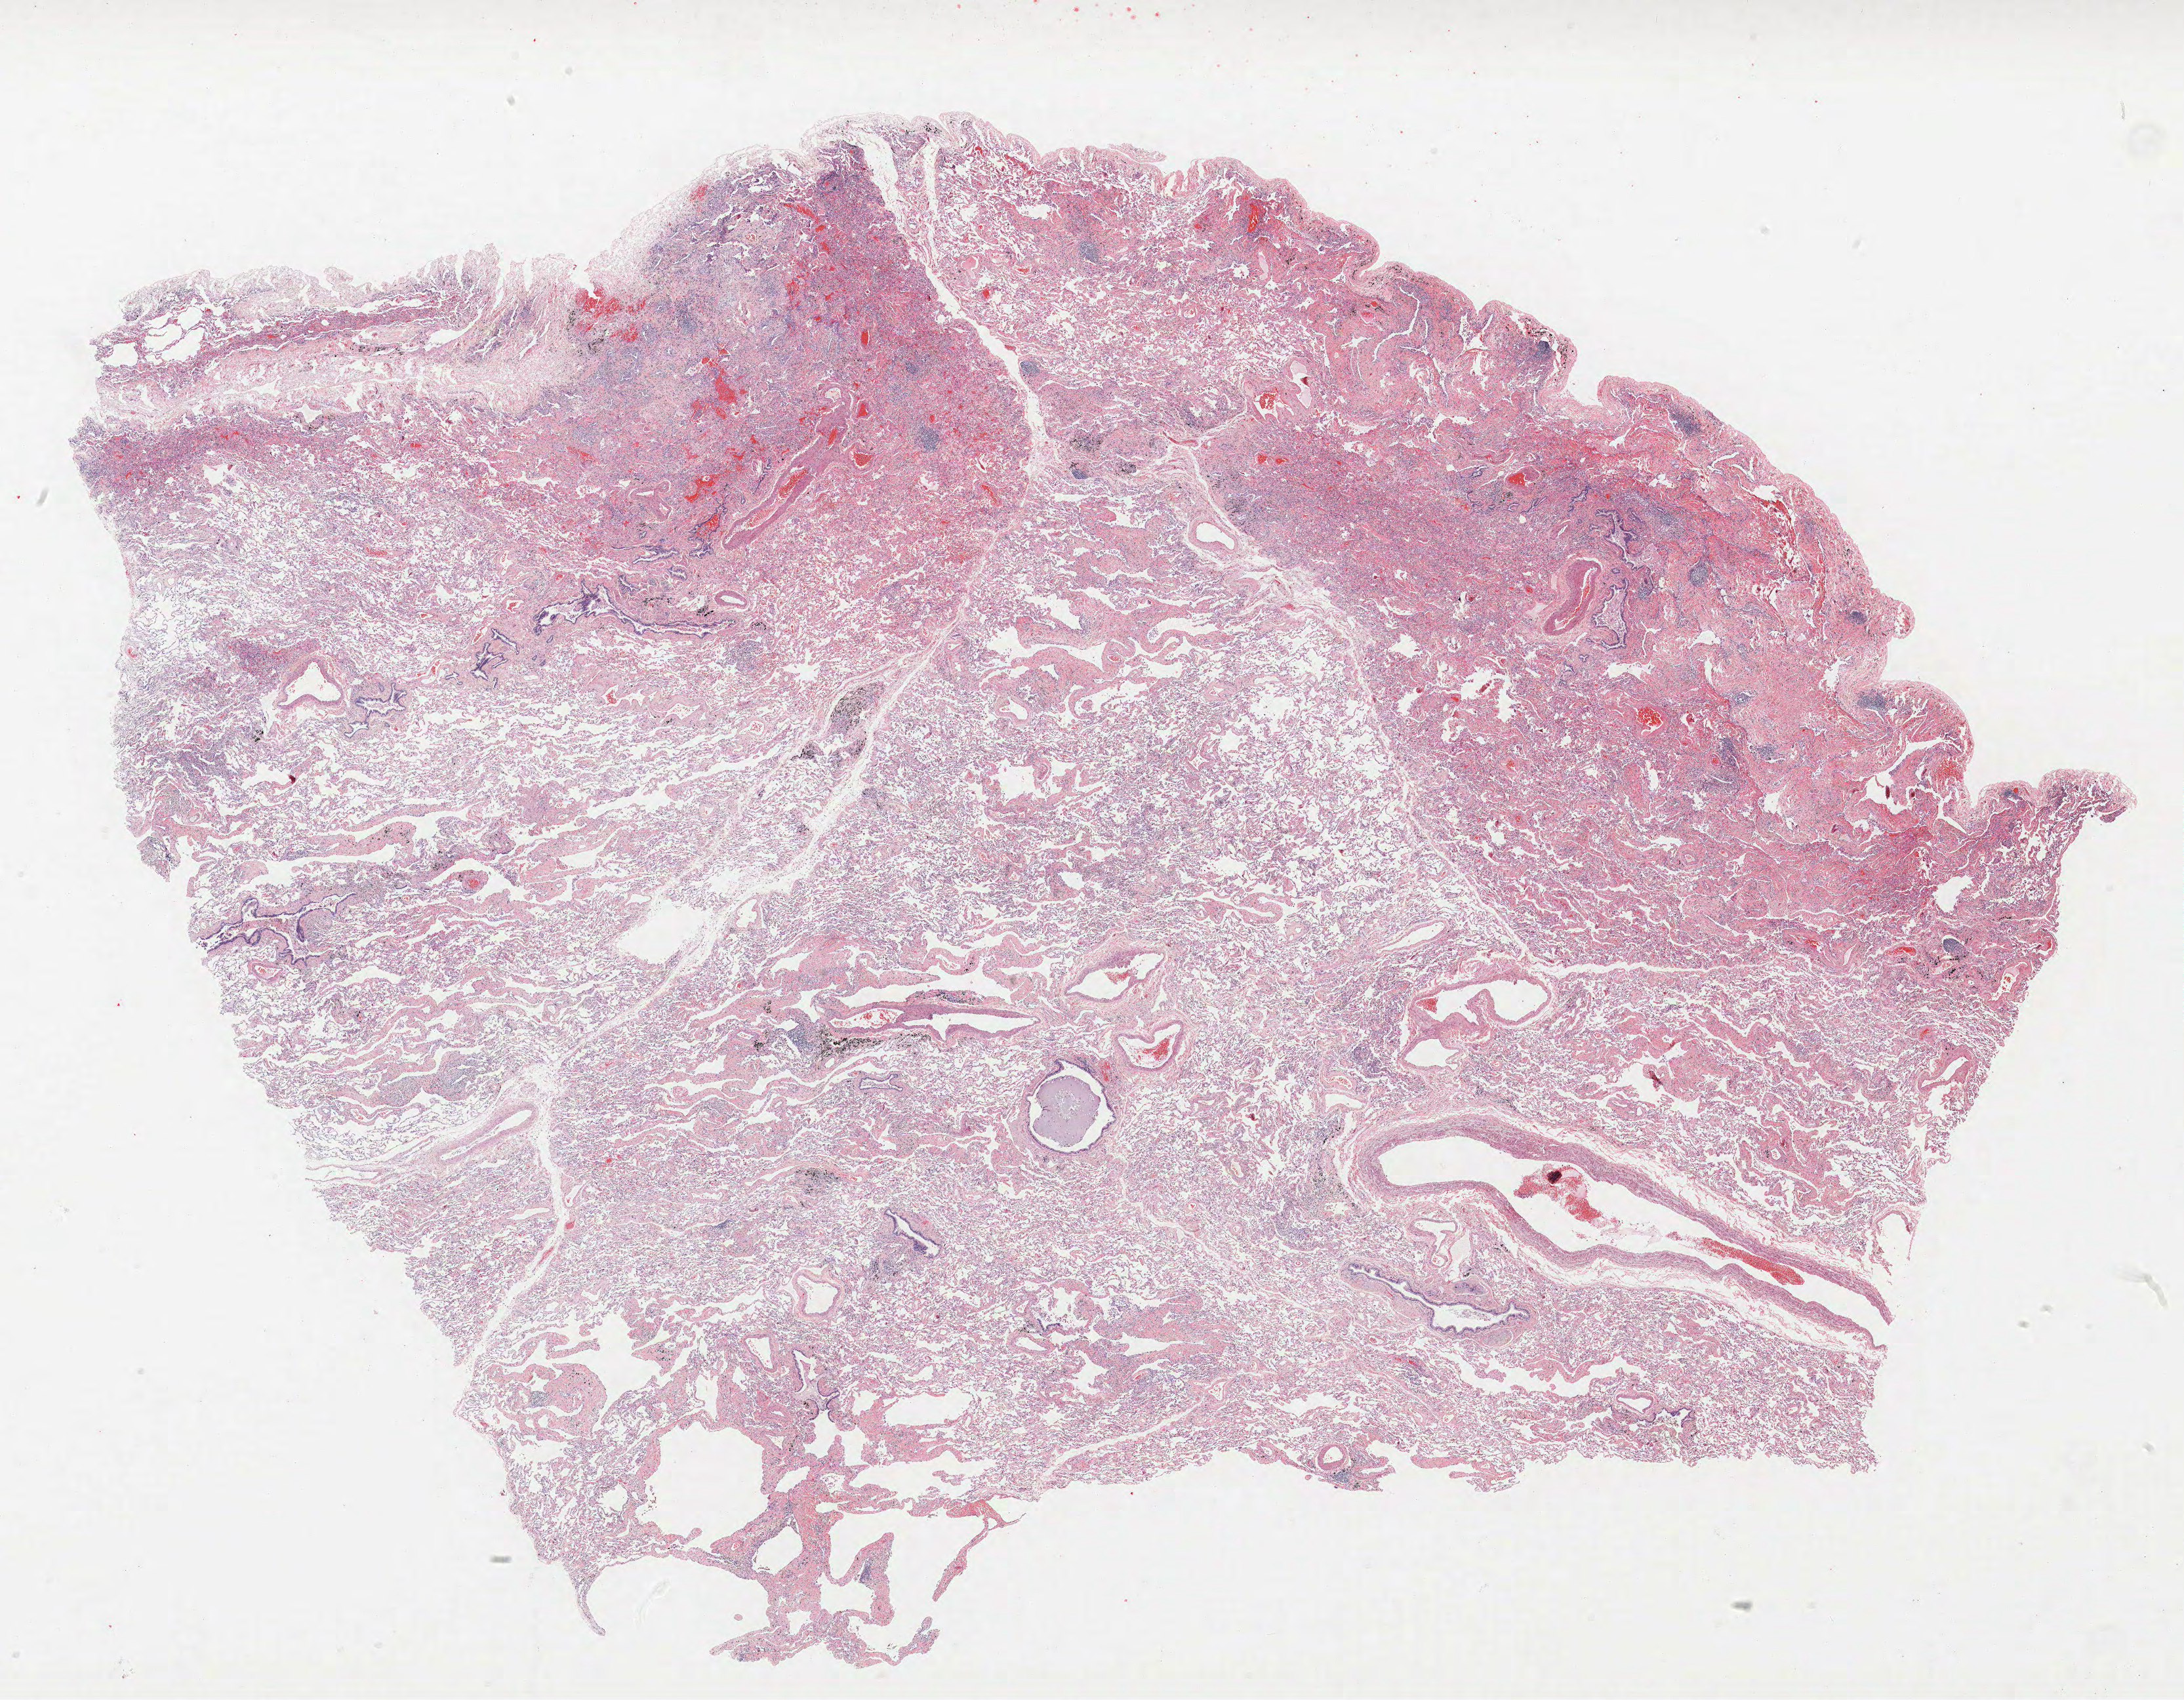
H&E whole-slide image — low-resolution overview of the scanned area, about 26.6 x 20.7 mm (acquisition: 40x scan); formalin-fixed paraffin-embedded (FFPE) section; lung. Male patient, aged 68 at enrolment. Current smoker at enrolment. Grade: undifferentiated (G4).
Tumour size (pathology): 25 mm. Participant's lung-cancer diagnosis: Large cell neuroendocrine carcinoma (ICD-O-3 8013/3). Stage (AJCC 6th edition): IA. Primary tumour location (clinical record): lingula. ICD-O-3 topography: upper lobe of lung (C34.1).